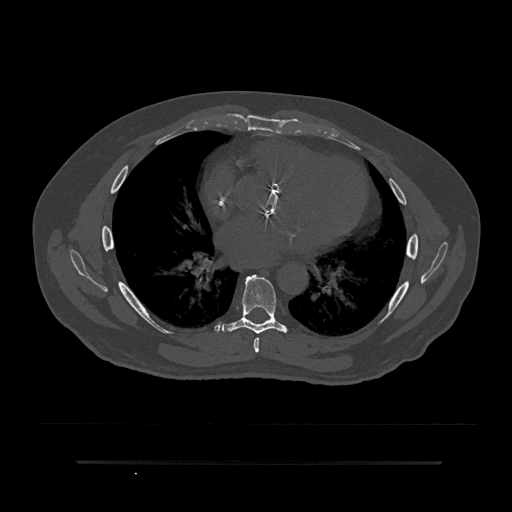
CT including the spine, one axial slice. Bone window (W 1800 / L 400 HU). 0.5 mm slice thickness. 512 × 512 image matrix, field of view 464 × 464 mm. Male patient, age 59 years. Case-level facts recorded for this patient, not image findings: primary cancer: bile ducts.
Structures marked on this image (semi-automatic segmentation, software-assisted and operator-edited):
- T6 vertebra: bounding box <253,337,260,353> (left, top, right, bottom; pixels)
- T7 vertebra: <222,274,288,334>